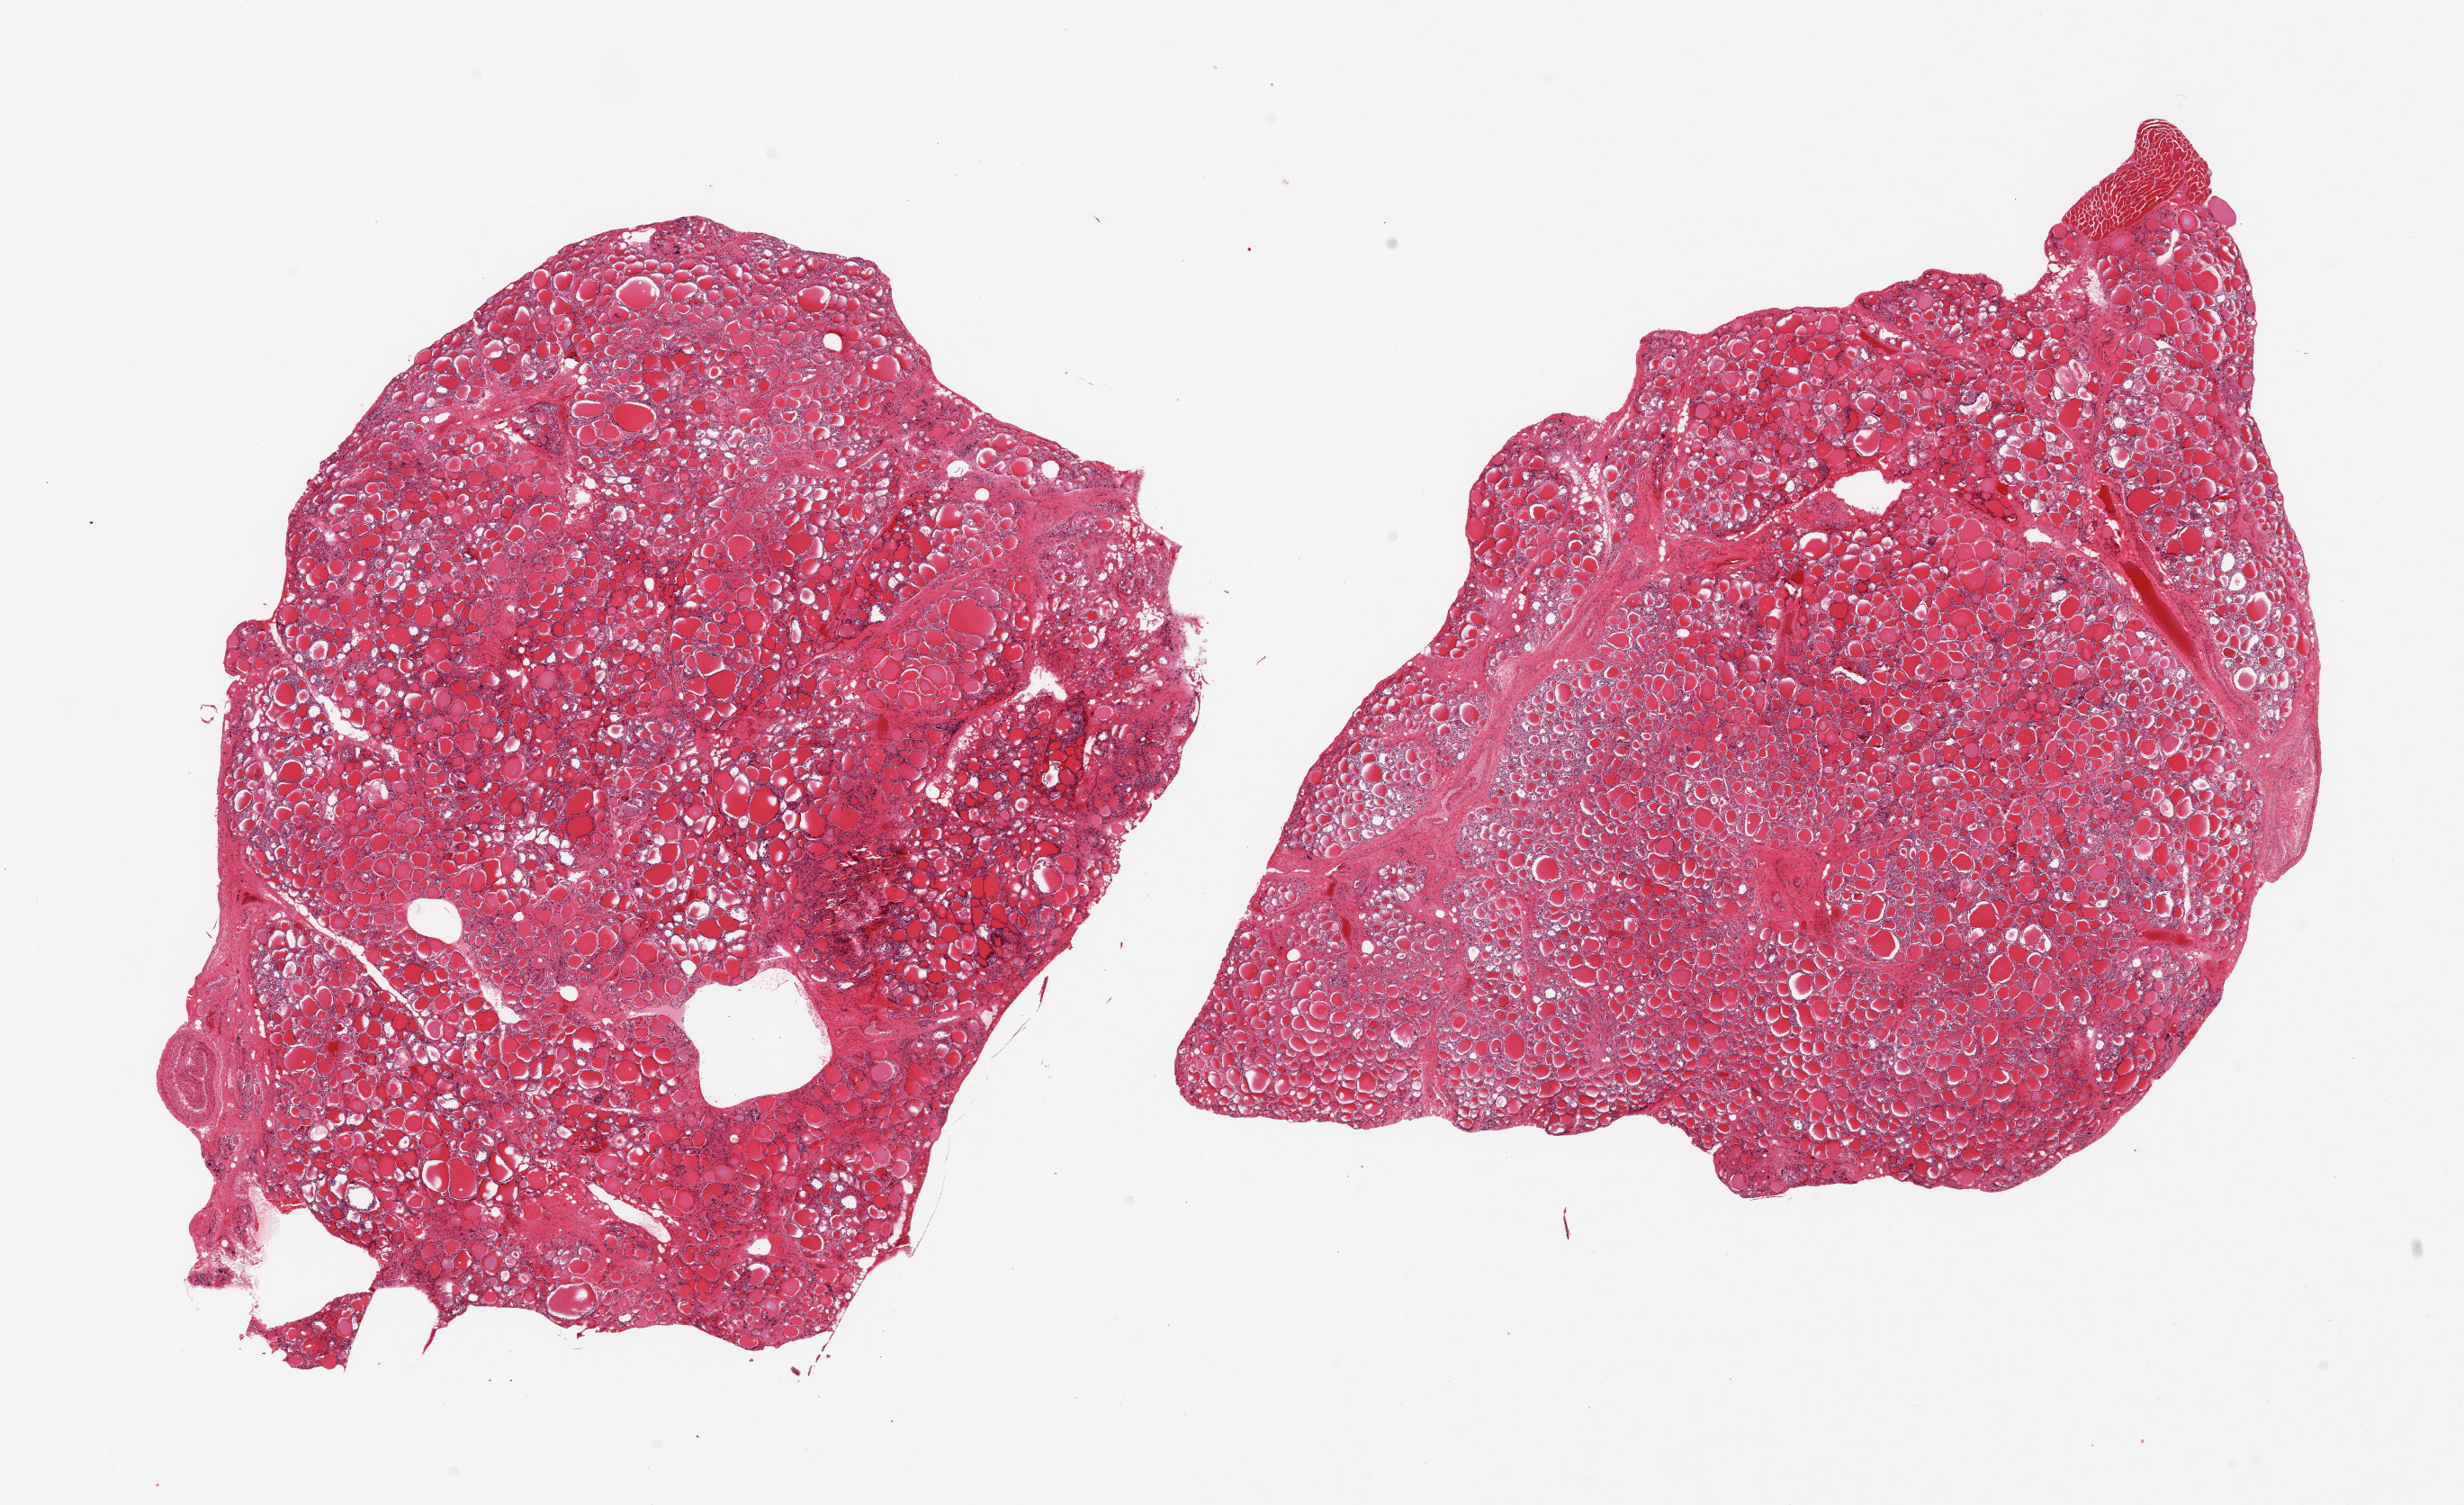
Digitized haematoxylin and eosin-stained section, brightfield — low-resolution overview of the scanned area, about 21.7 x 13.2 mm, PAXgene-fixed paraffin-embedded (PFPE) section, sampled site (target tissue): thyroid, tissue donor sample. Donor sex: female.
Pathologist's review note for this sample: 2 pieces, mild goitre.